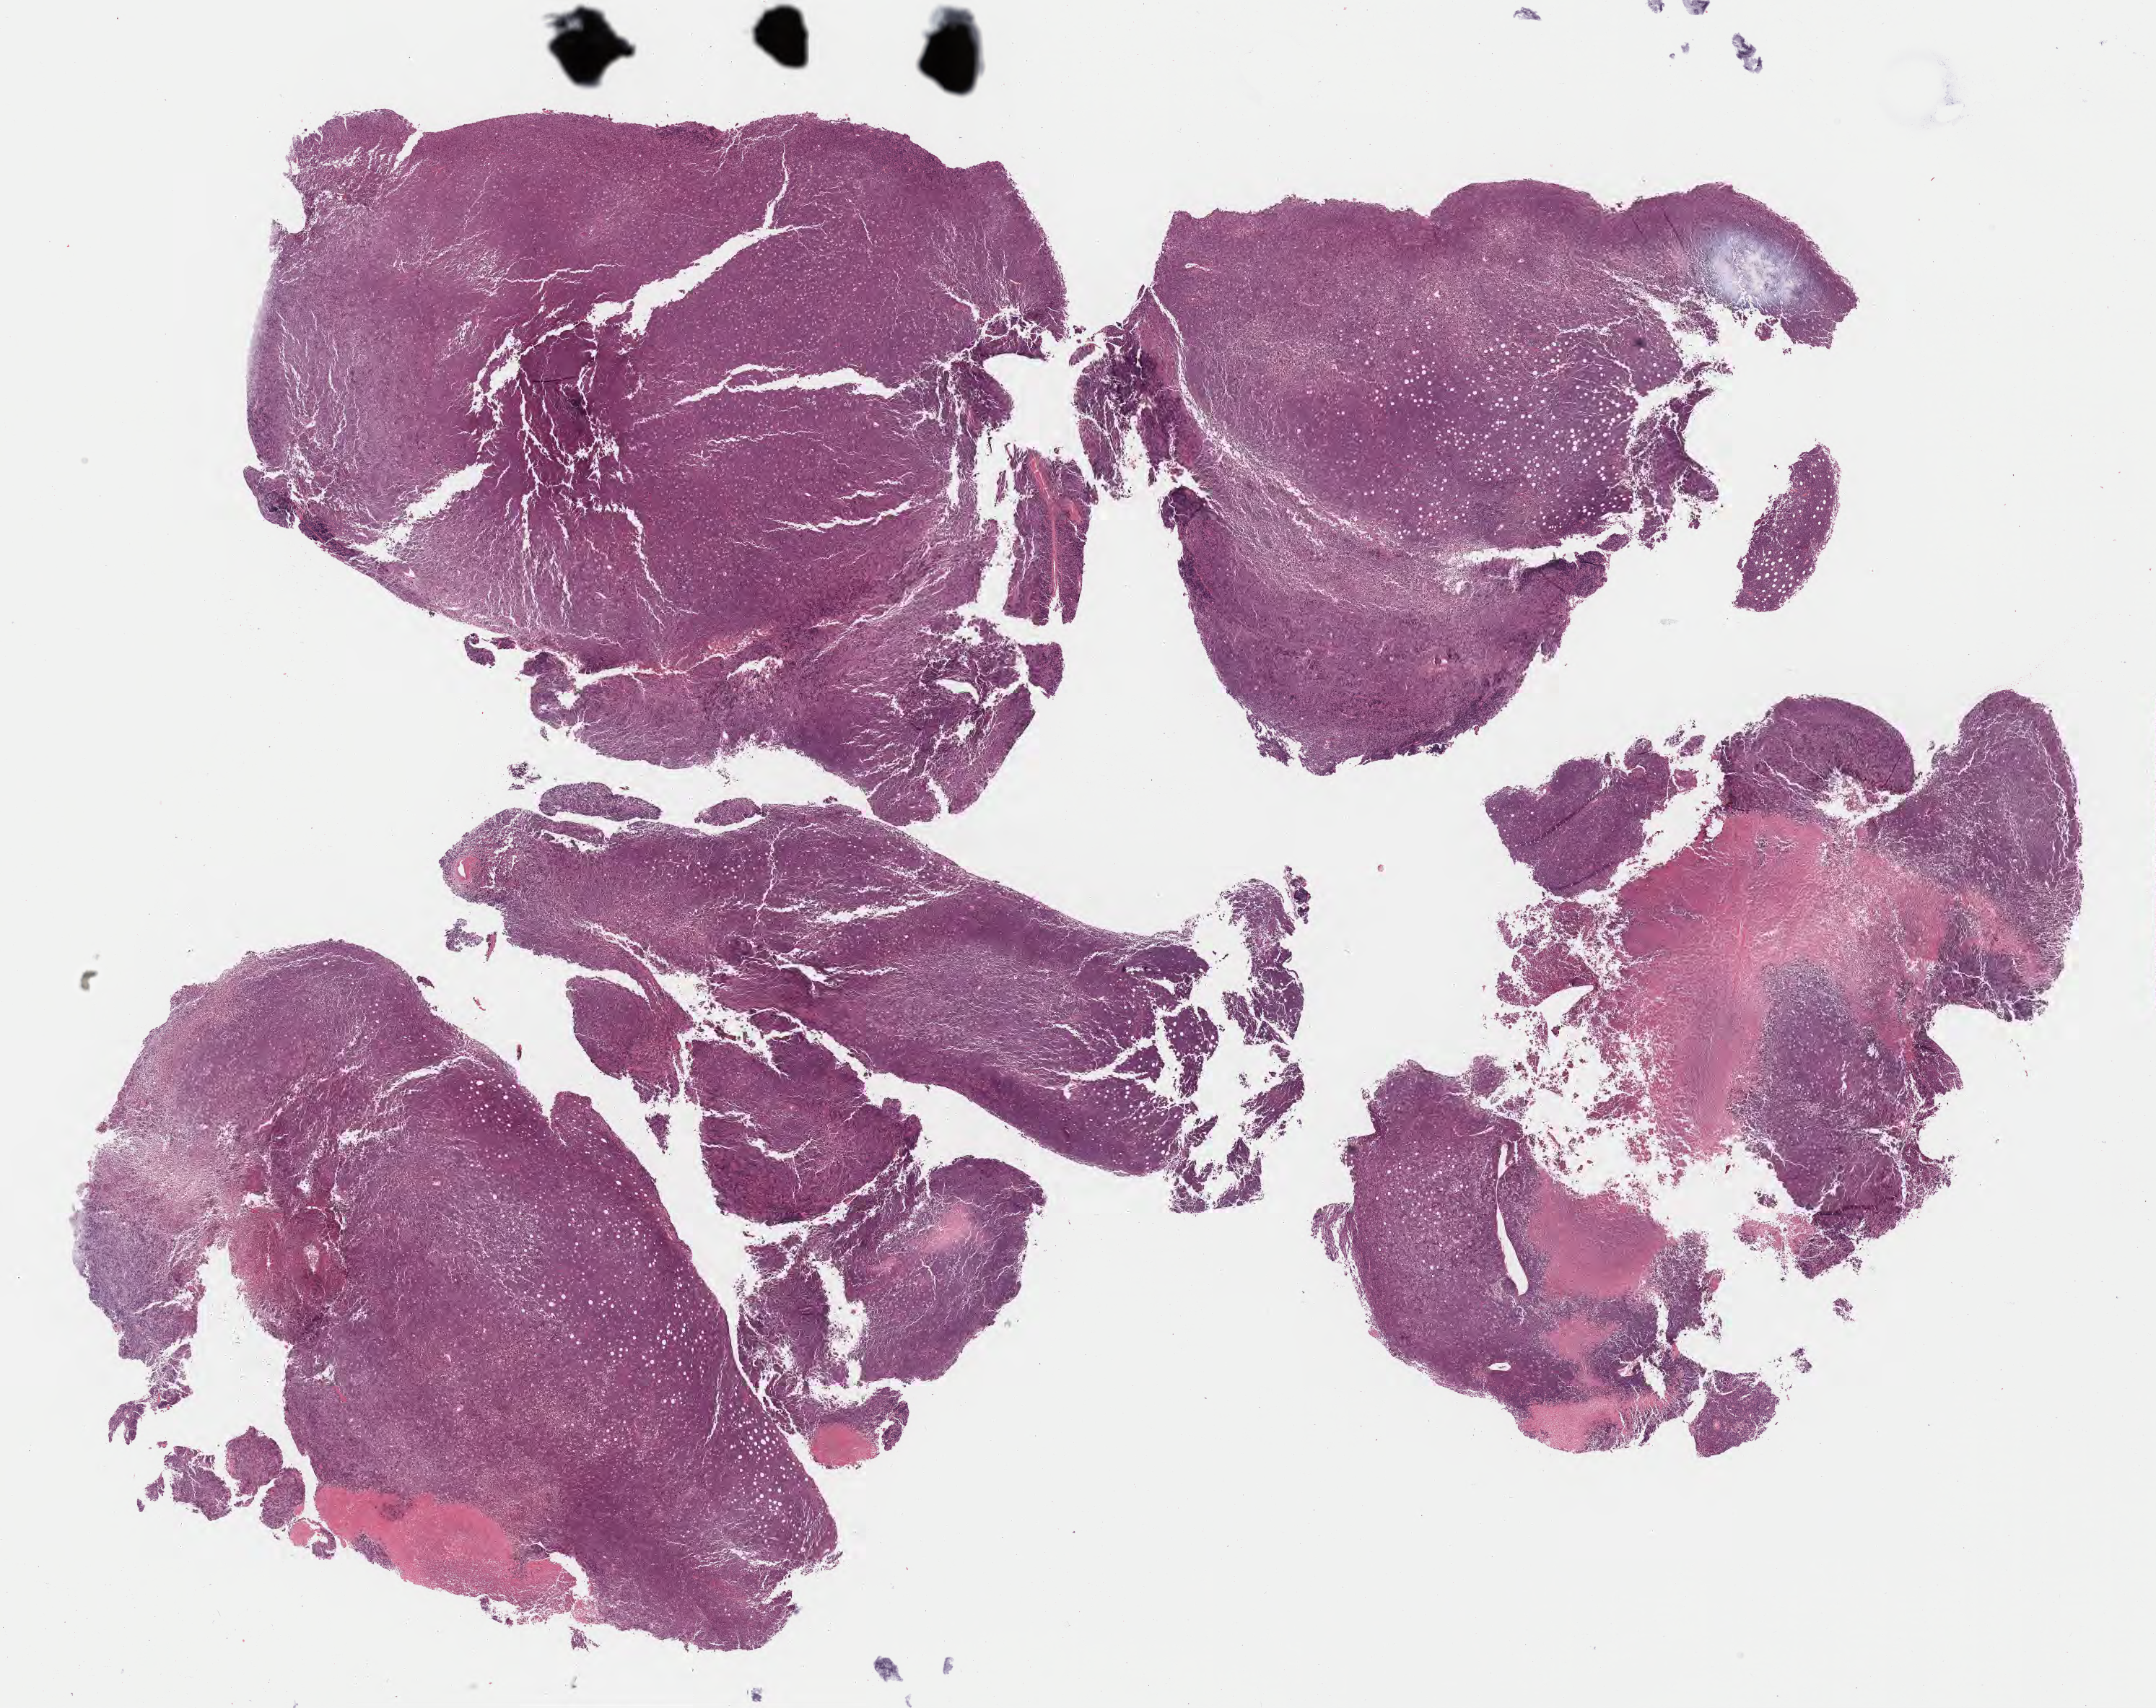
Haematoxylin and eosin whole-slide image — low-resolution overview of the scanned area, about 24.2 x 19.1 mm; specimen: tumor tissue. Patient: male, age 60 years.
Histologic diagnosis: Diffuse large B-cell lymphoma, NOS.